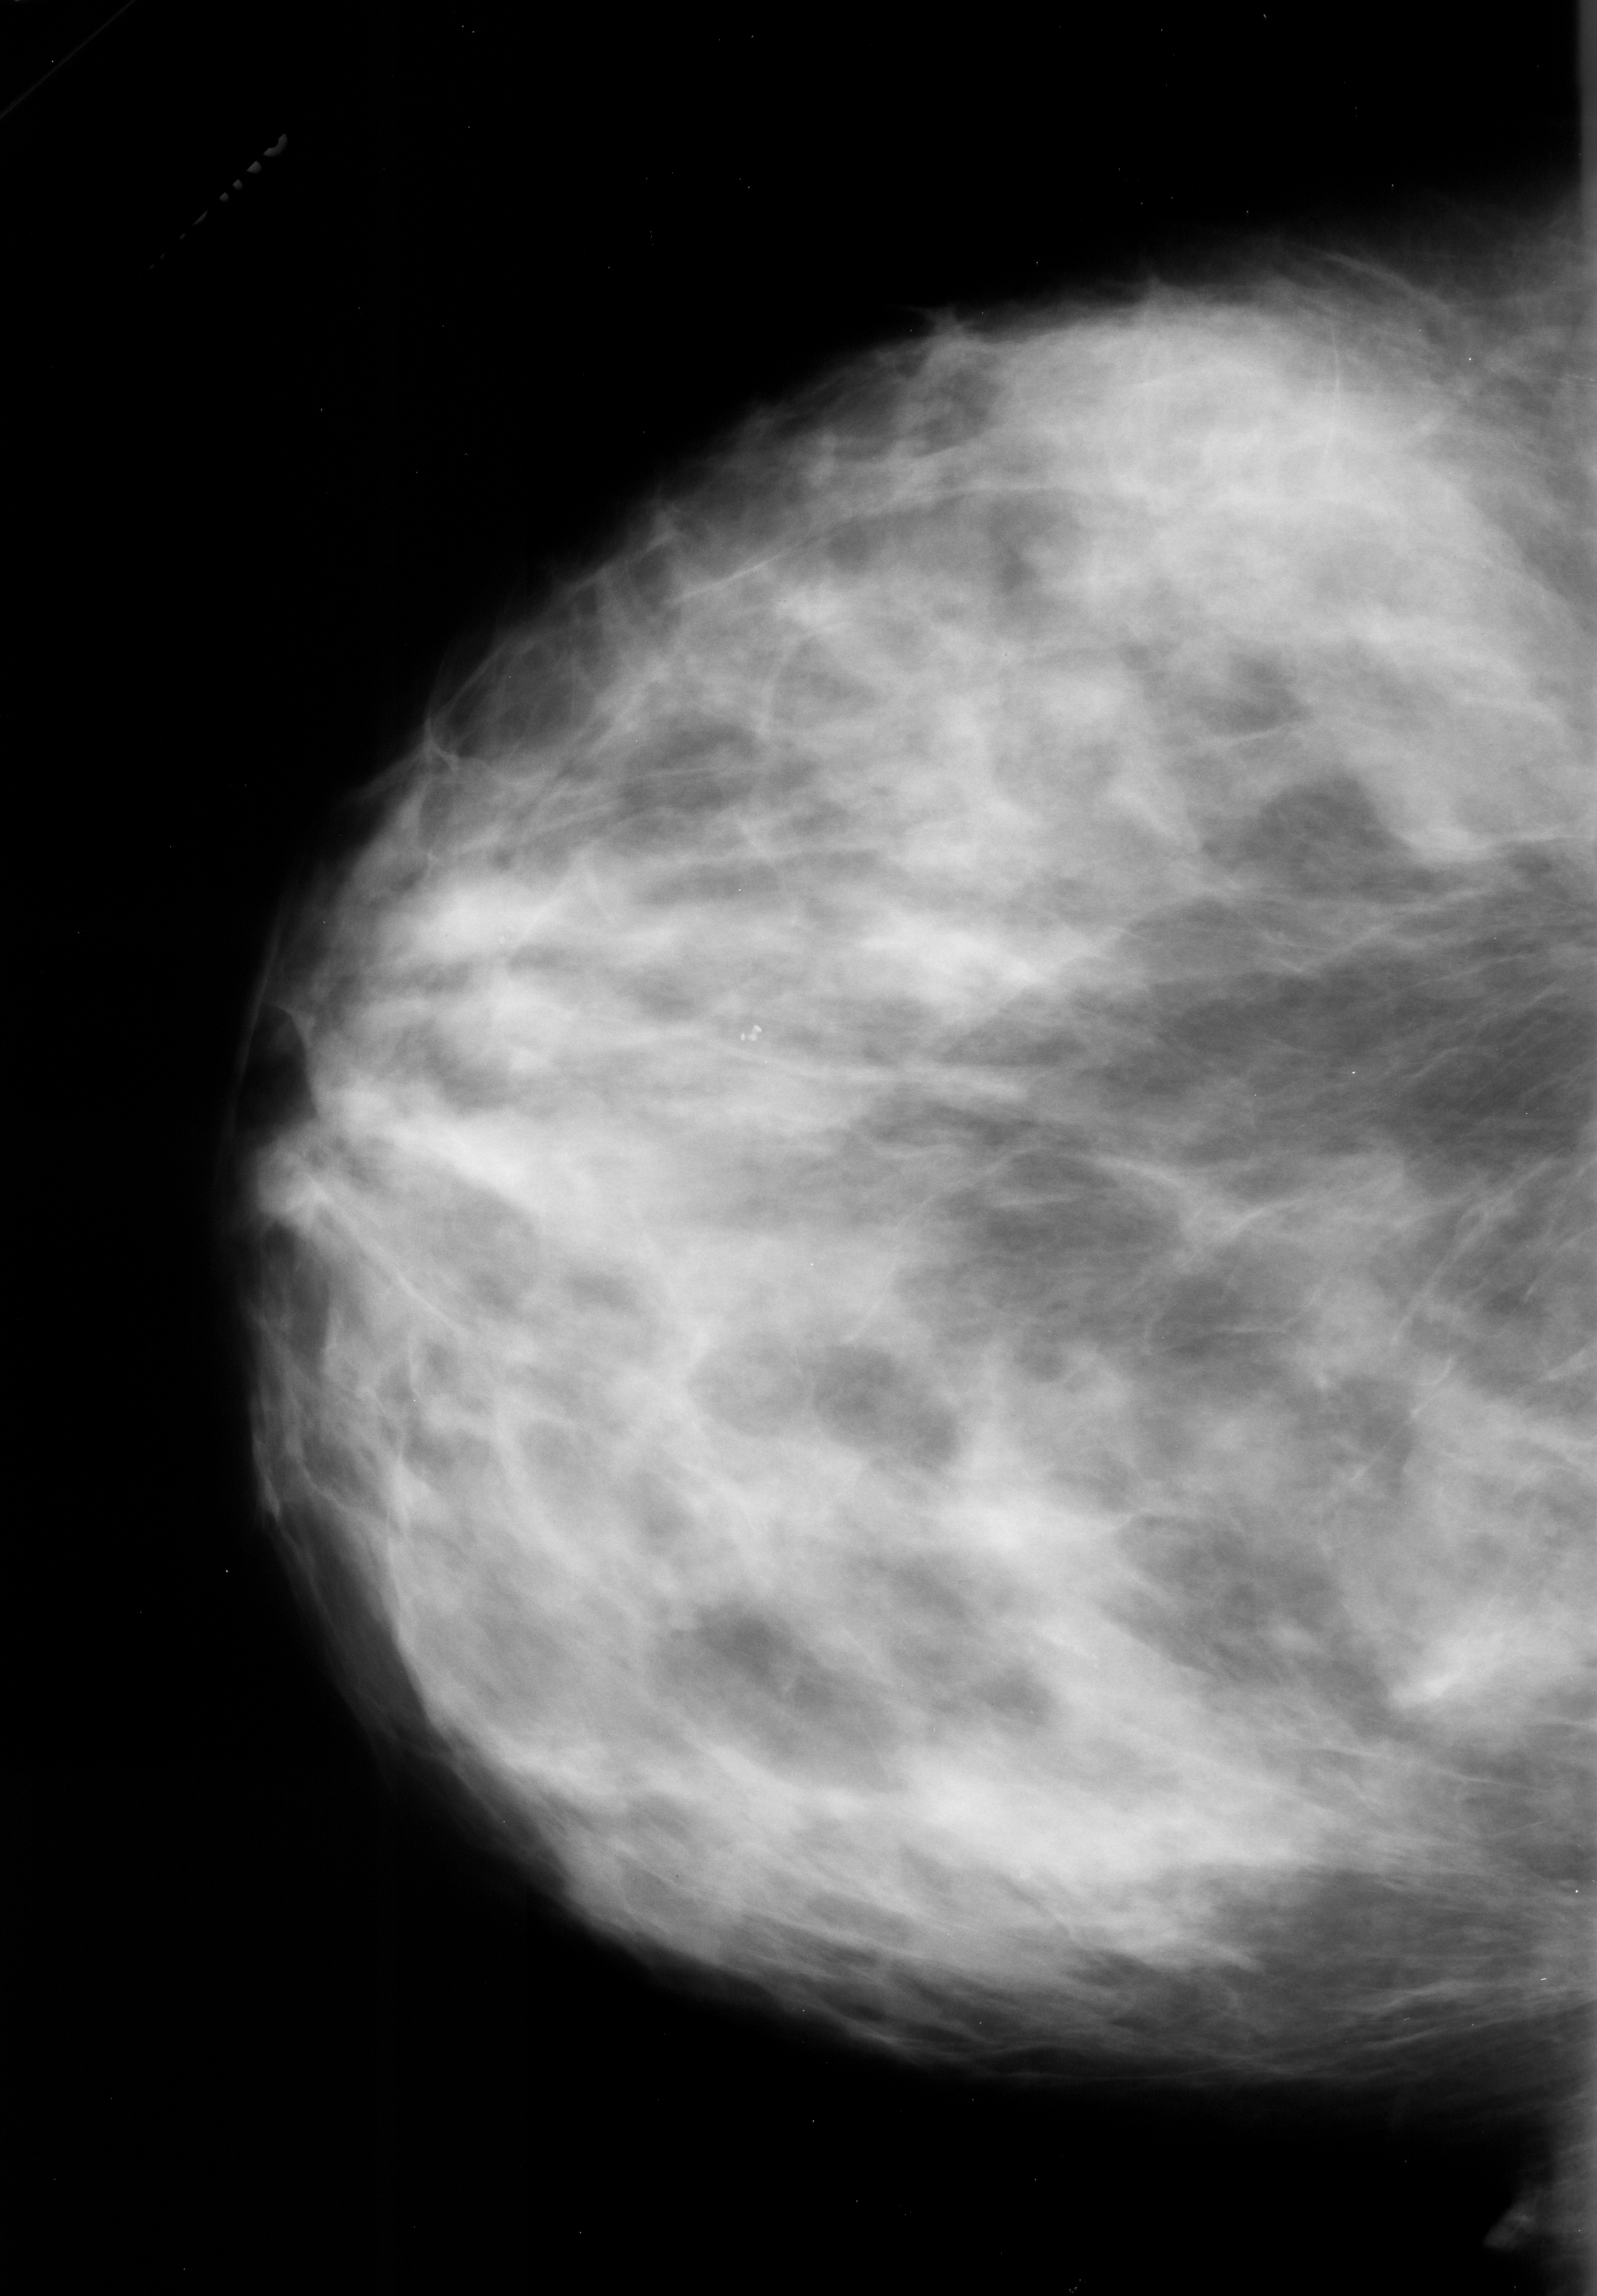
Mammogram (digitized film). Left breast. CC view. 1597 × 2296 image matrix.
Expert-marked regions of interest on this image (one box per marked abnormality):
- calcifications, morphology pleomorphic, distribution linear; BI-RADS assessment category 4; pathology result (as recorded, not read from the image): malignant: bounding box <1032,1616,1128,1674> (left, top, right, bottom; pixels)